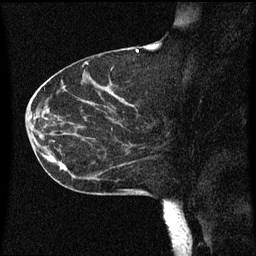
Breast MRI (dynamic contrast-enhanced), one sagittal slice; slice 26 of 60 in the series (ordered by position); dynamic contrast-enhanced series, image 2 of 3 at this slice position (ordered by acquisition); 1.5 T; TE 4.2 ms, TR 8 ms; 2 mm slice thickness; 256 × 256 image matrix. Female patient, age 55 years.
Outlined on this slice (semi-automatically segmented with operator editing):
- analysis volume of interest (the breast-tissue region the enhancement analysis was run in; not a lesion): bounding box [x1, y1, x2, y2] px = [46, 124, 151, 183]
- tumour enhancement mask (voxels above the 70 % enhancement threshold inside the analysis volume of interest): [50, 156, 103, 173]